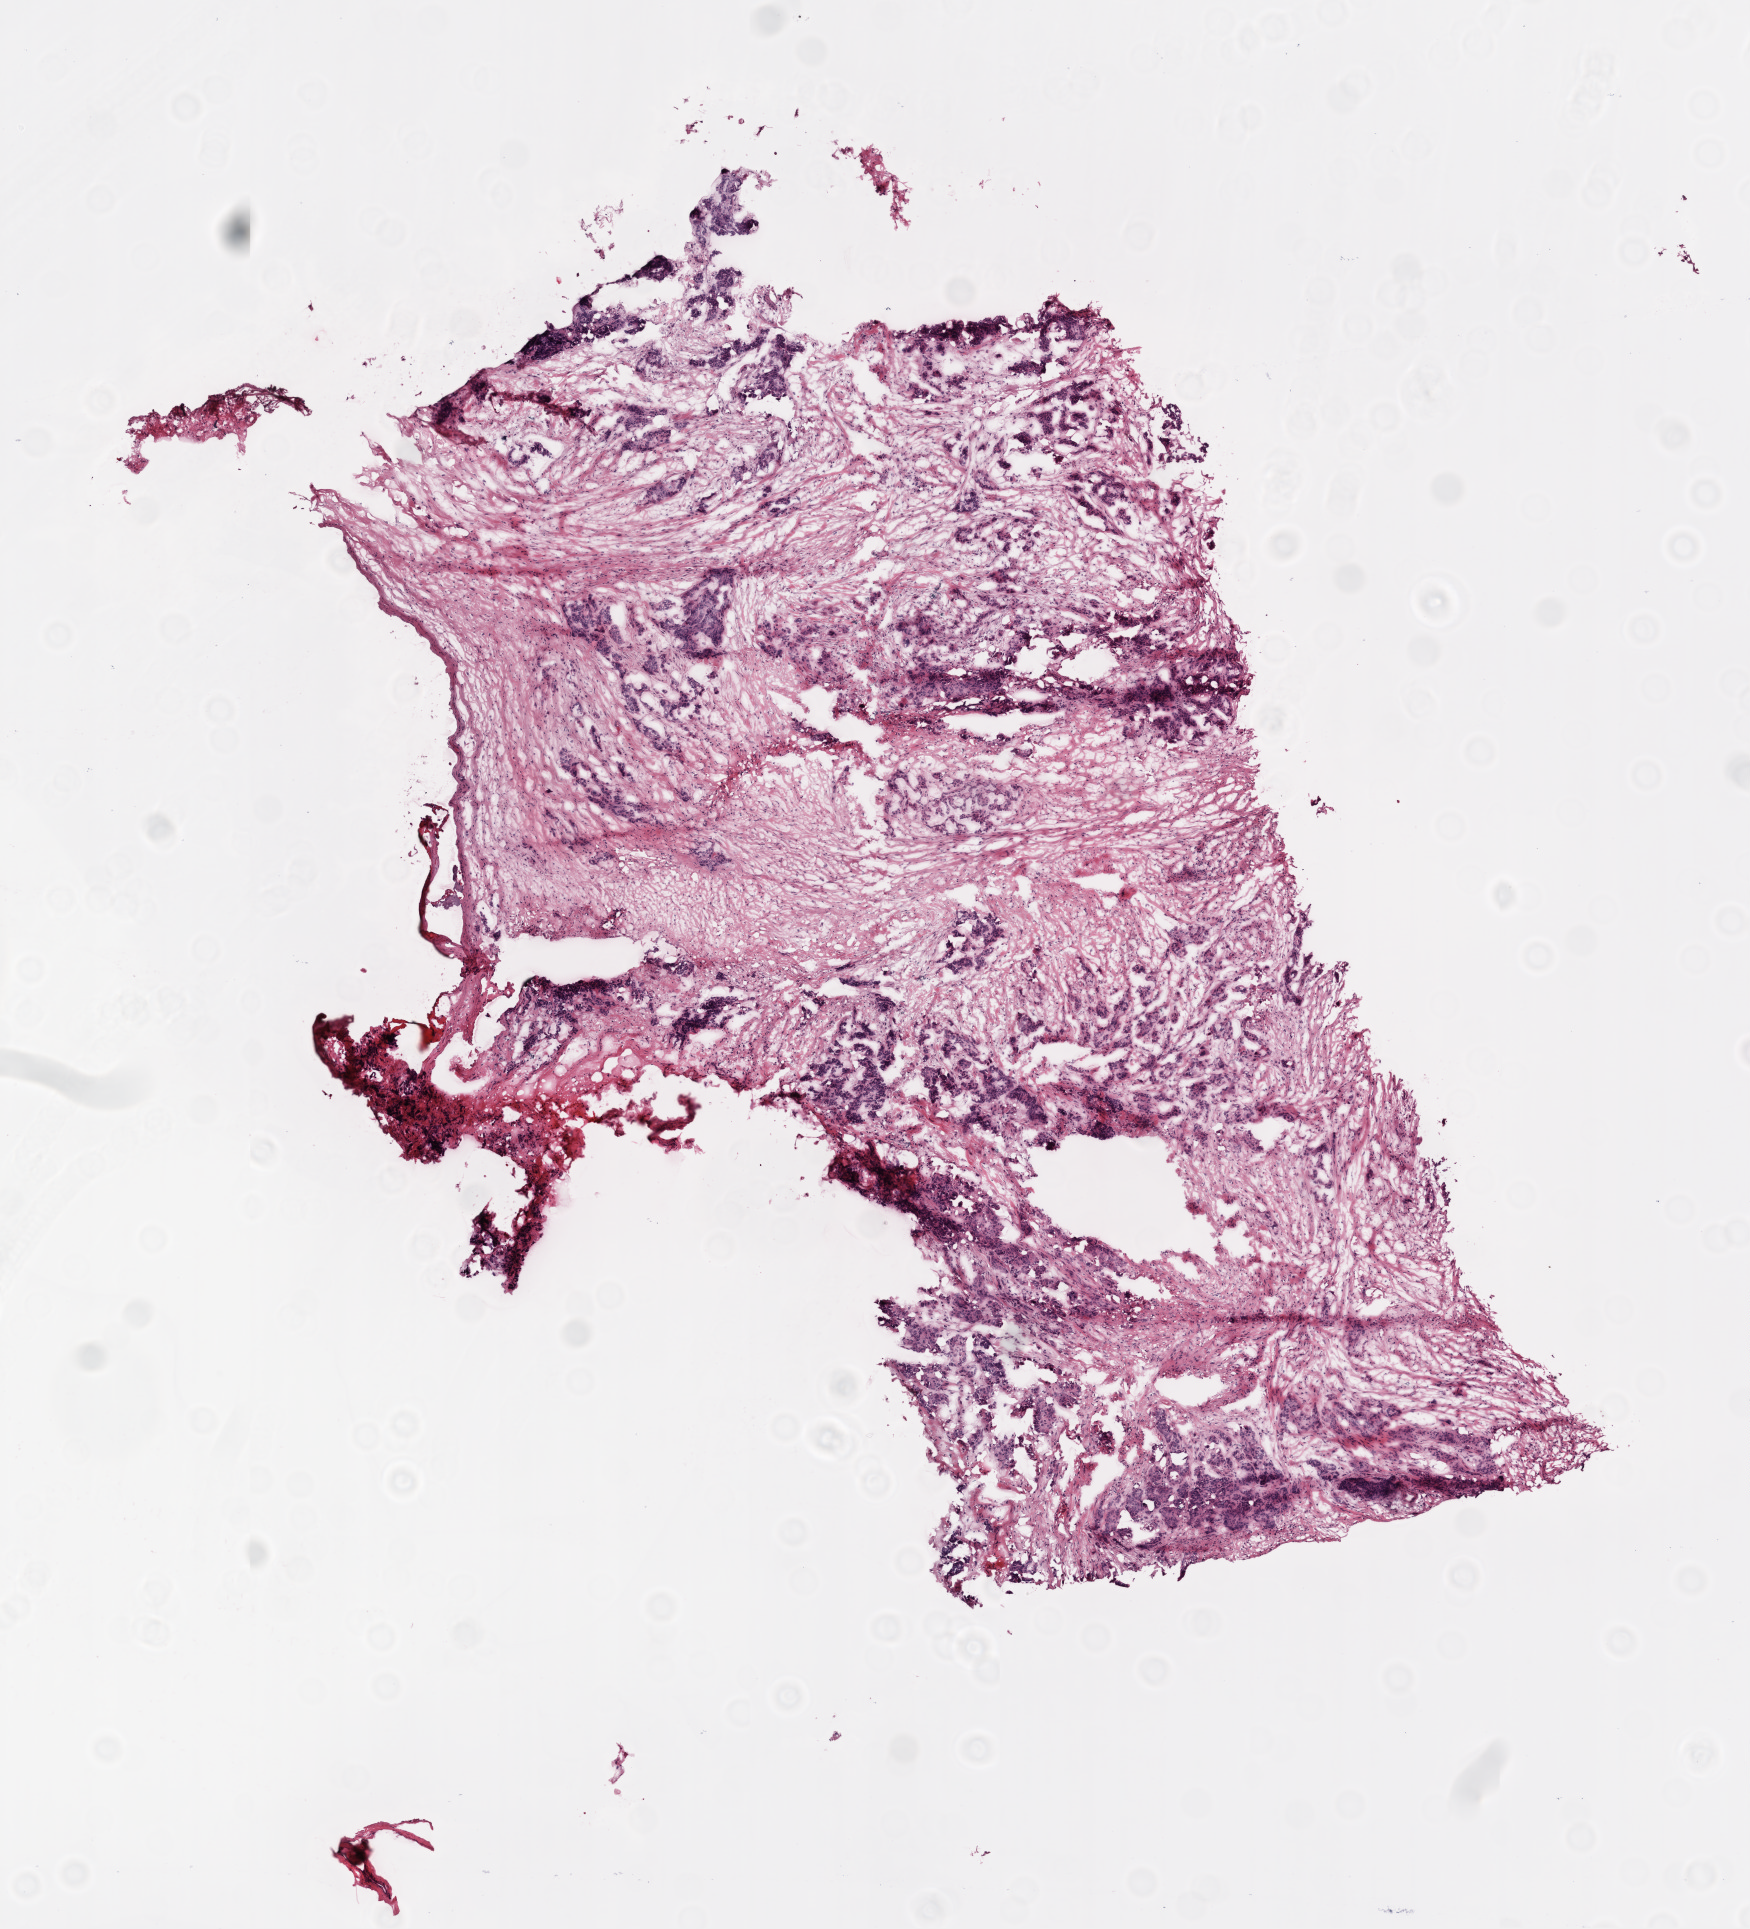
H&E-stained whole-slide image — whole scanned area (about 7.0 x 7.7 mm) shown as a low-resolution overview. Frozen section from the top of the tissue portion. Ovary, recurrent tumour sample. Patient: female, age at initial diagnosis 47 years.
This section: recurrent tumour. Patient diagnosis: Serous cystadenocarcinoma, NOS.